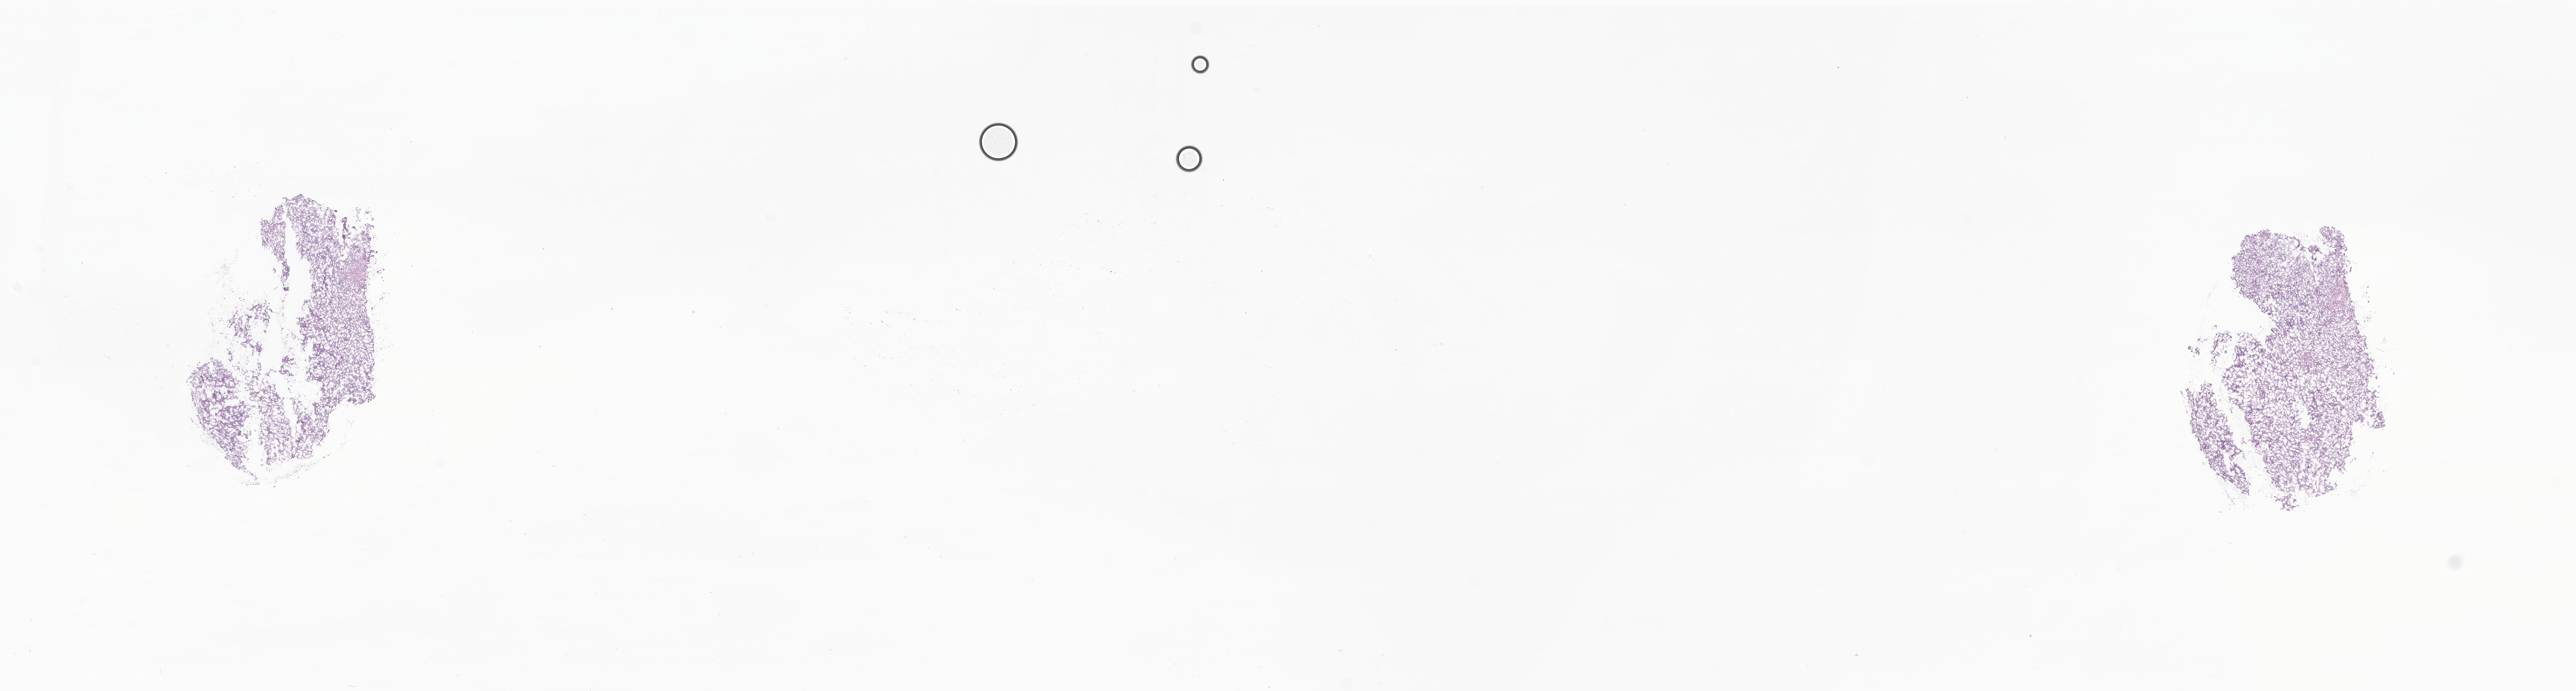
Whole-slide image, haematoxylin and eosin stain of tumor tissue from the brain, shown as a low-resolution overview of the whole scanned area (about 26.4 x 7.1 mm); frozen section (OCT-embedded). Patient: female, age 158 months (13 years 2 months).
• diagnosis (ICD-O-3 morphology term): Pilocytic astrocytoma